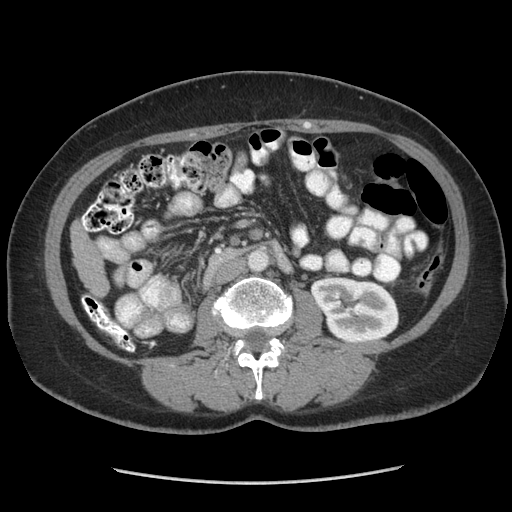
Contrast-enhanced abdominal CT (liver protocol), one axial slice. Position 112 of 185 along the scan axis. Reconstruction kernel STANDARD. 140 kVp. Soft-tissue window (W 400 / L 40 HU). 2.5 mm slice thickness. 512 × 512 image matrix, field of view 360 × 360 mm. From the clinical record (not read from this slice): diagnosis: hepatocellular carcinoma (patient treated with transarterial chemoembolisation; whether this scan precedes or follows treatment is not stated here); TNM stage (as recorded): Stage-I; Child-Pugh class: A; tumour differentiation: poorly differentiated; tumour nodularity: uninodular.
Annotated regions visible in this slice (semi-automatically segmented with operator editing):
- liver parenchyma outside the tumour (the mass and vessels are separate outlines, so this box may not span the whole liver): bounding box (x1, y1, x2, y2) in pixels: (72, 219, 108, 296)
- liver vessels: (83, 219, 87, 229)